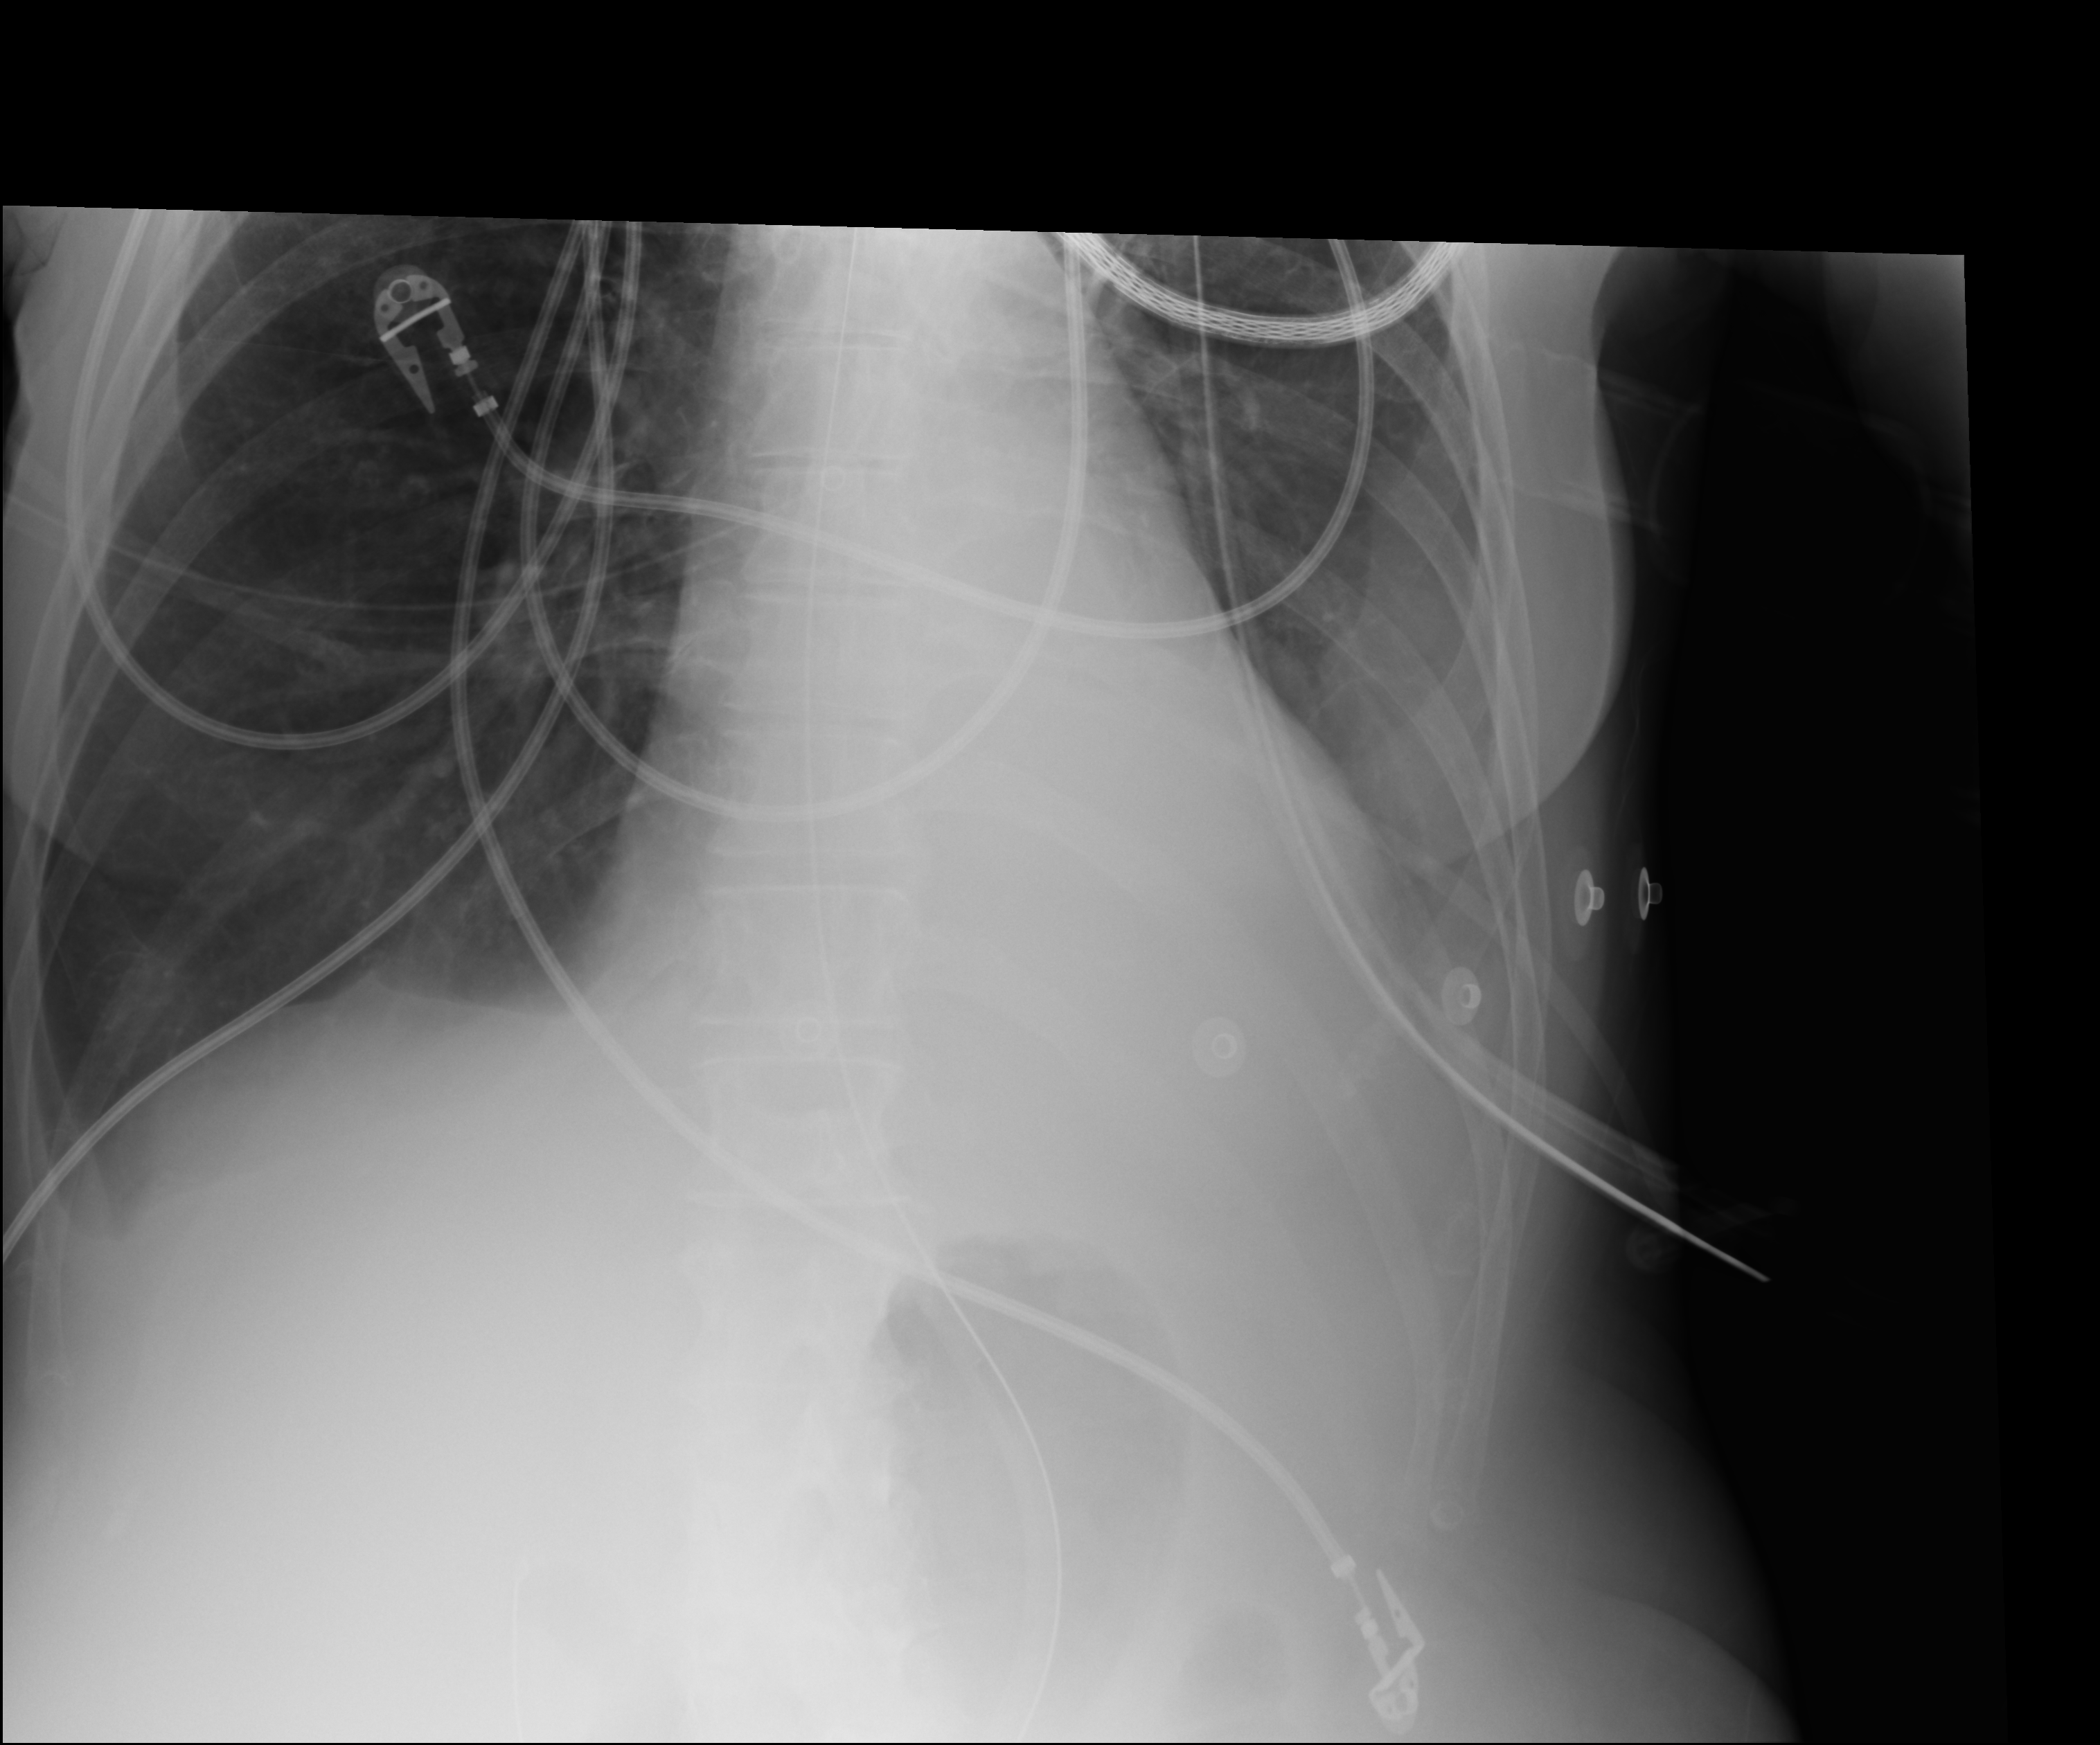
Portable chest radiograph; anteroposterior (AP) projection. Female patient hospitalised with COVID-19, age 60–74 years.
Admission-level facts for this patient (not findings on this image; timing relative to this image not recorded): admitted to intensive care during this hospital stay: yes.